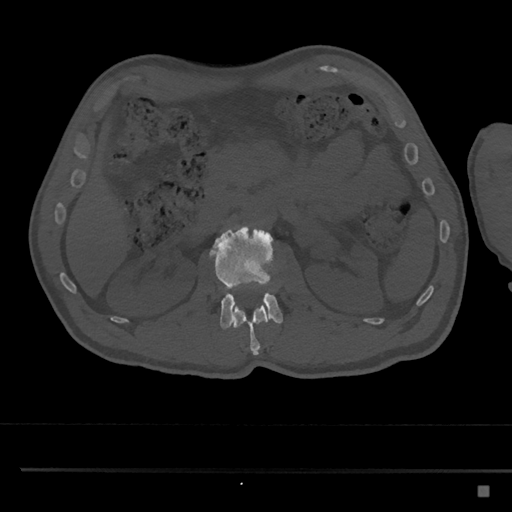
CT including the spine, one axial slice; slice 790 of 797 in the series (ordered by position); 120 kVp; bone window (W 1800 / L 400 HU); 0.5 mm slice thickness; 512 × 512 image matrix, field of view 391 × 391 mm. Male patient, age 59 years. From the clinical record (not read from this slice): primary cancer: prostate.
Annotated regions visible in this slice (semi-automatic segmentation, software-assisted and operator-edited):
- L1 vertebra: box from (x=233, y=300) to (x=269, y=356) px
- L2 vertebra: (x=208, y=226)–(x=283, y=329)